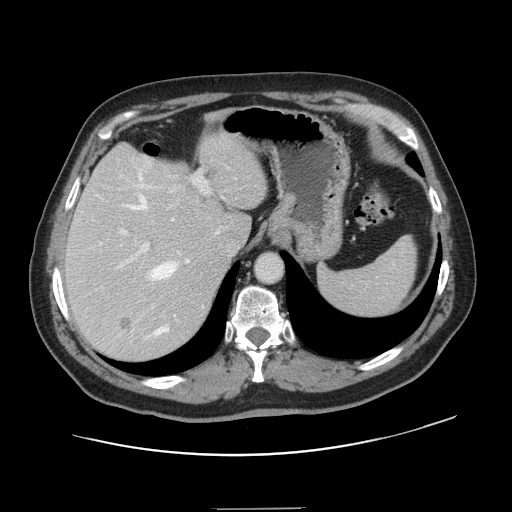
Contrast-enhanced abdominal CT, one axial slice; position 106 of 143 along the scan axis; 120 kVp; intravenous contrast given; soft-tissue window (W 400 / L 40 HU); 2.5 mm slice thickness; 512 × 512 image matrix. Male patient, age 62 years. From the clinical record (not read from this slice): diagnosis: colorectal cancer liver metastases, imaged before liver resection.
Structures marked on this image (expert manual segmentation):
- hepatic veins: box from (x=100, y=170) to (x=189, y=339) px
- liver: (x=66, y=131)–(x=267, y=360)
- planned liver remnant (the part of the liver to remain after resection): (x=66, y=131)–(x=266, y=271)
- portal vein (with intrahepatic branches): (x=120, y=171)–(x=209, y=277)
- liver metastasis: (x=118, y=318)–(x=135, y=333)
- liver metastasis: (x=162, y=170)–(x=176, y=185)